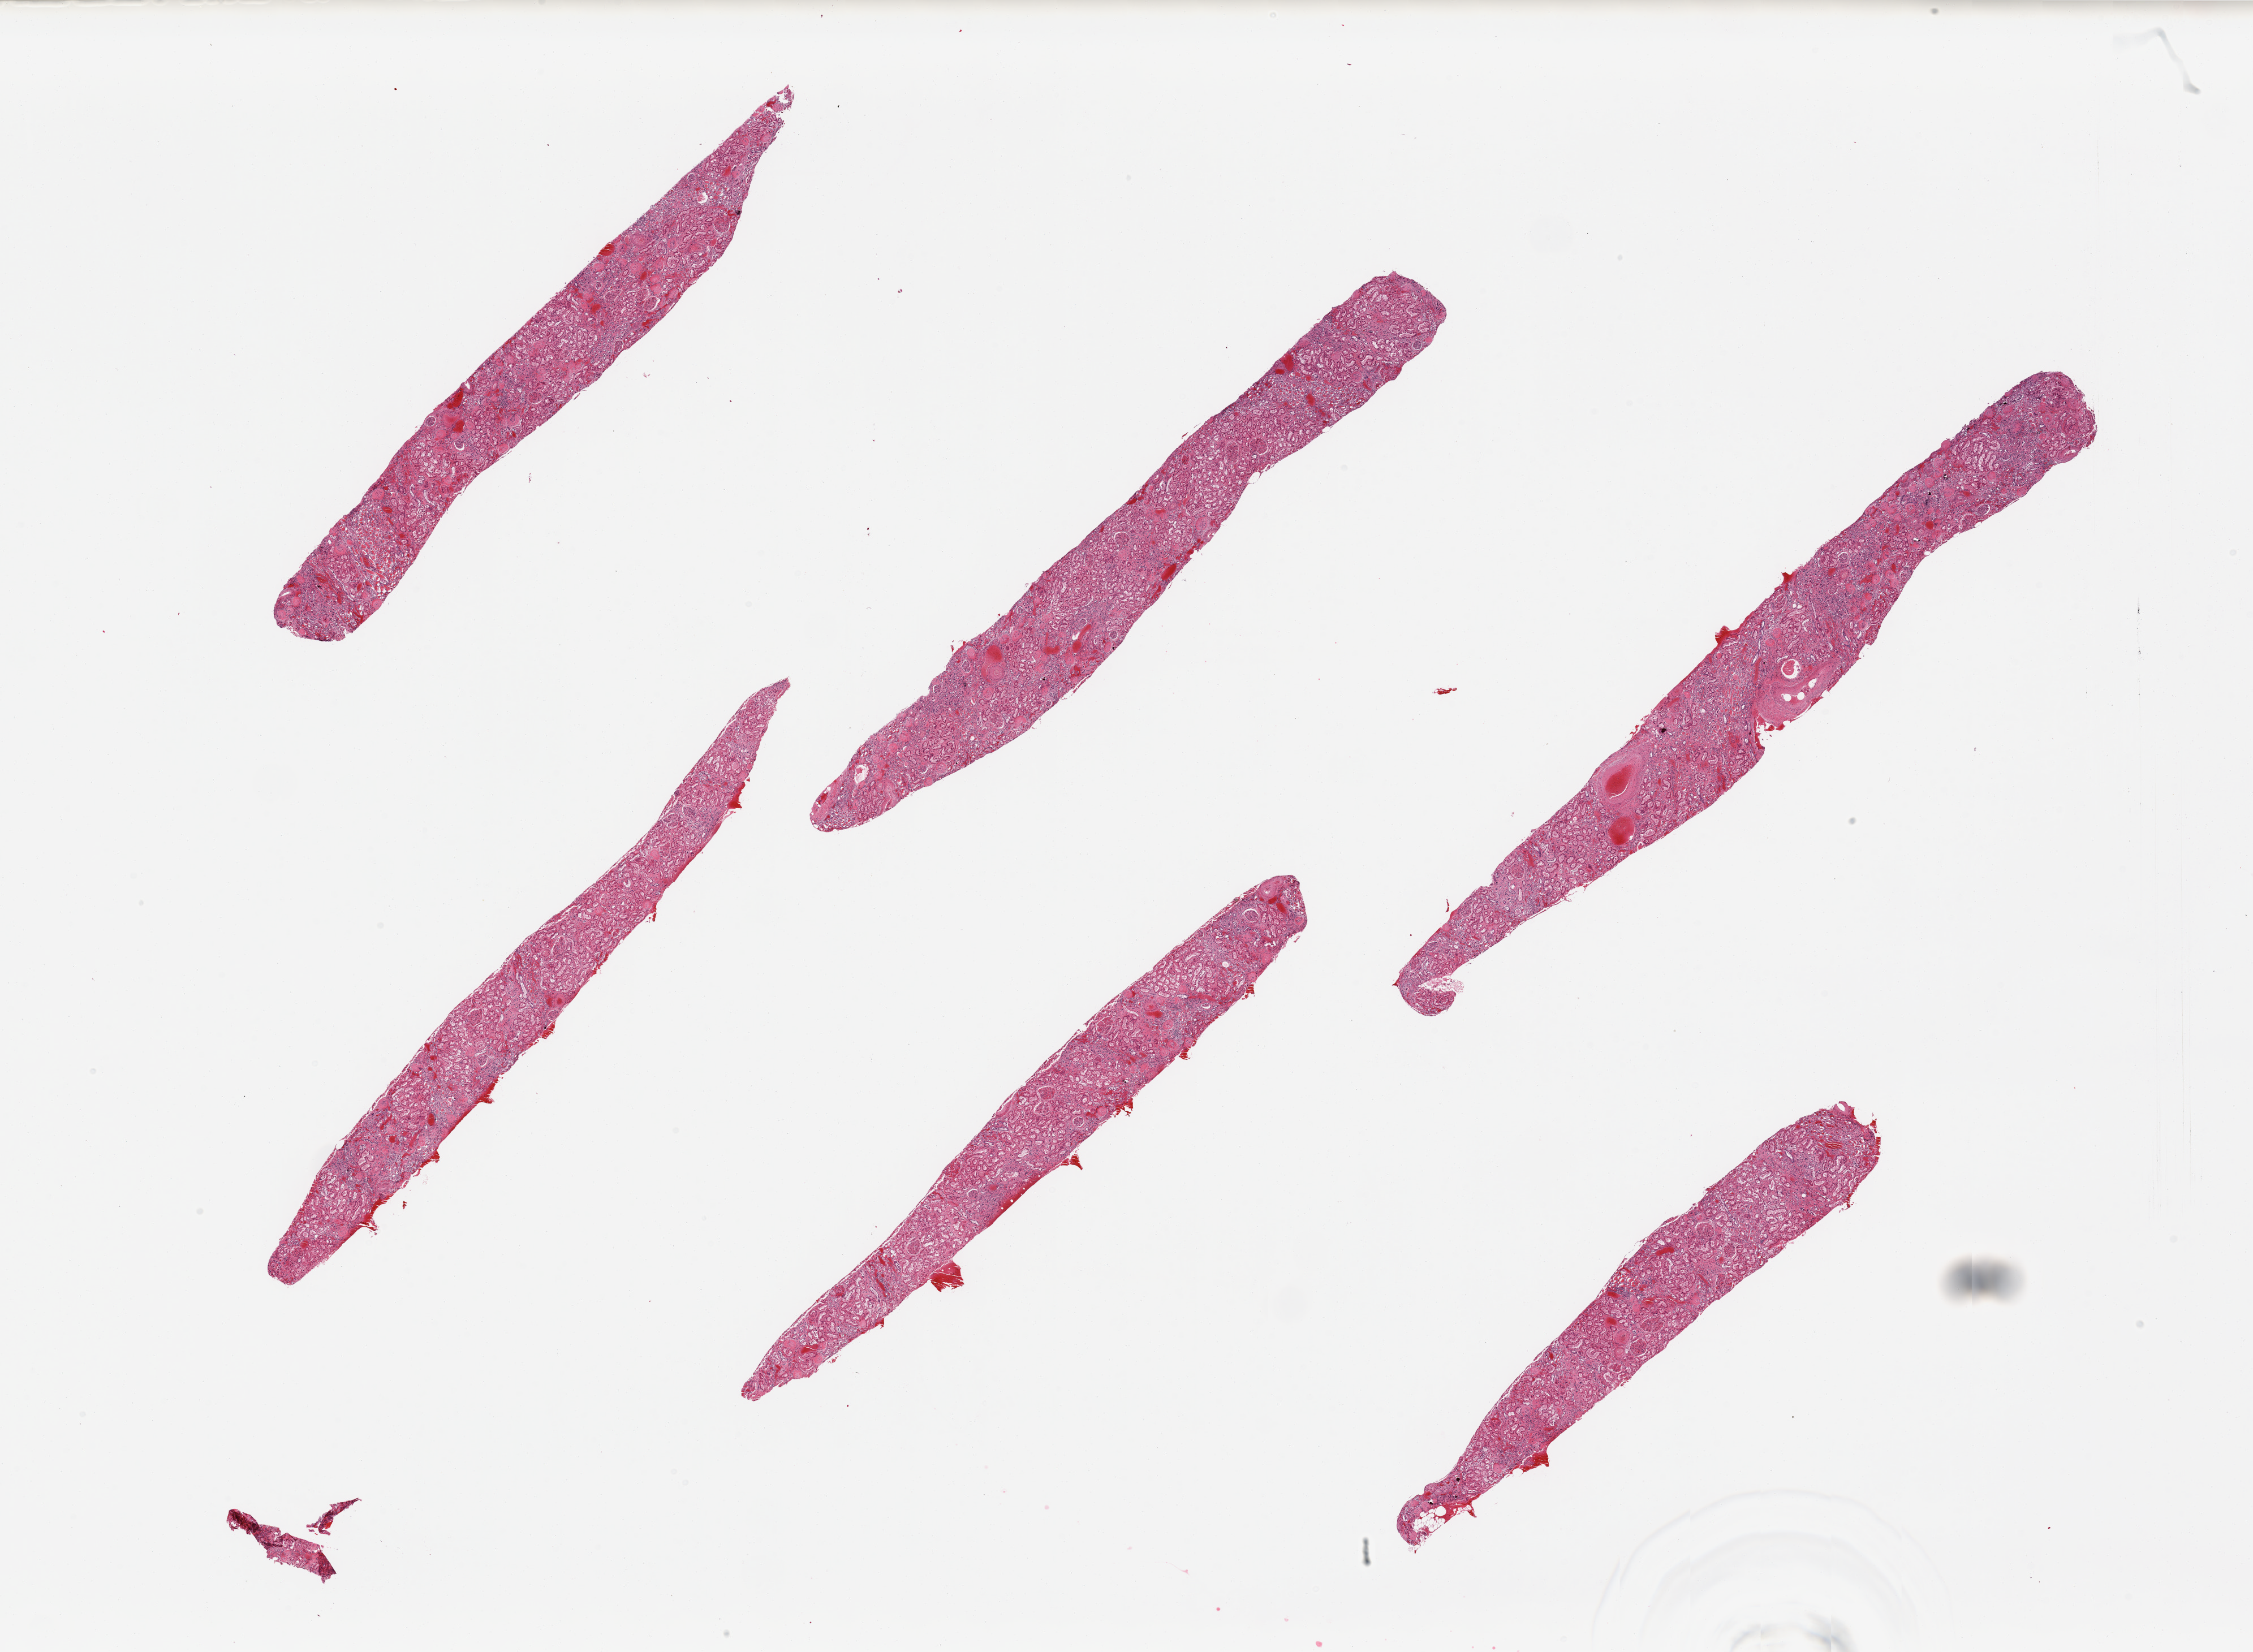
Whole-slide image, haematoxylin and eosin stain, shown as a low-resolution overview of the whole scanned area (about 31.5 x 23.1 mm, acquisition: 20x scan), PAXgene-fixed, paraffin-embedded tissue, sampled site (target tissue): renal cortex, donor tissue sample. Donor sex: male.
Review note (as recorded): 6 pieces, glomerulie present; tubules autolyzed.